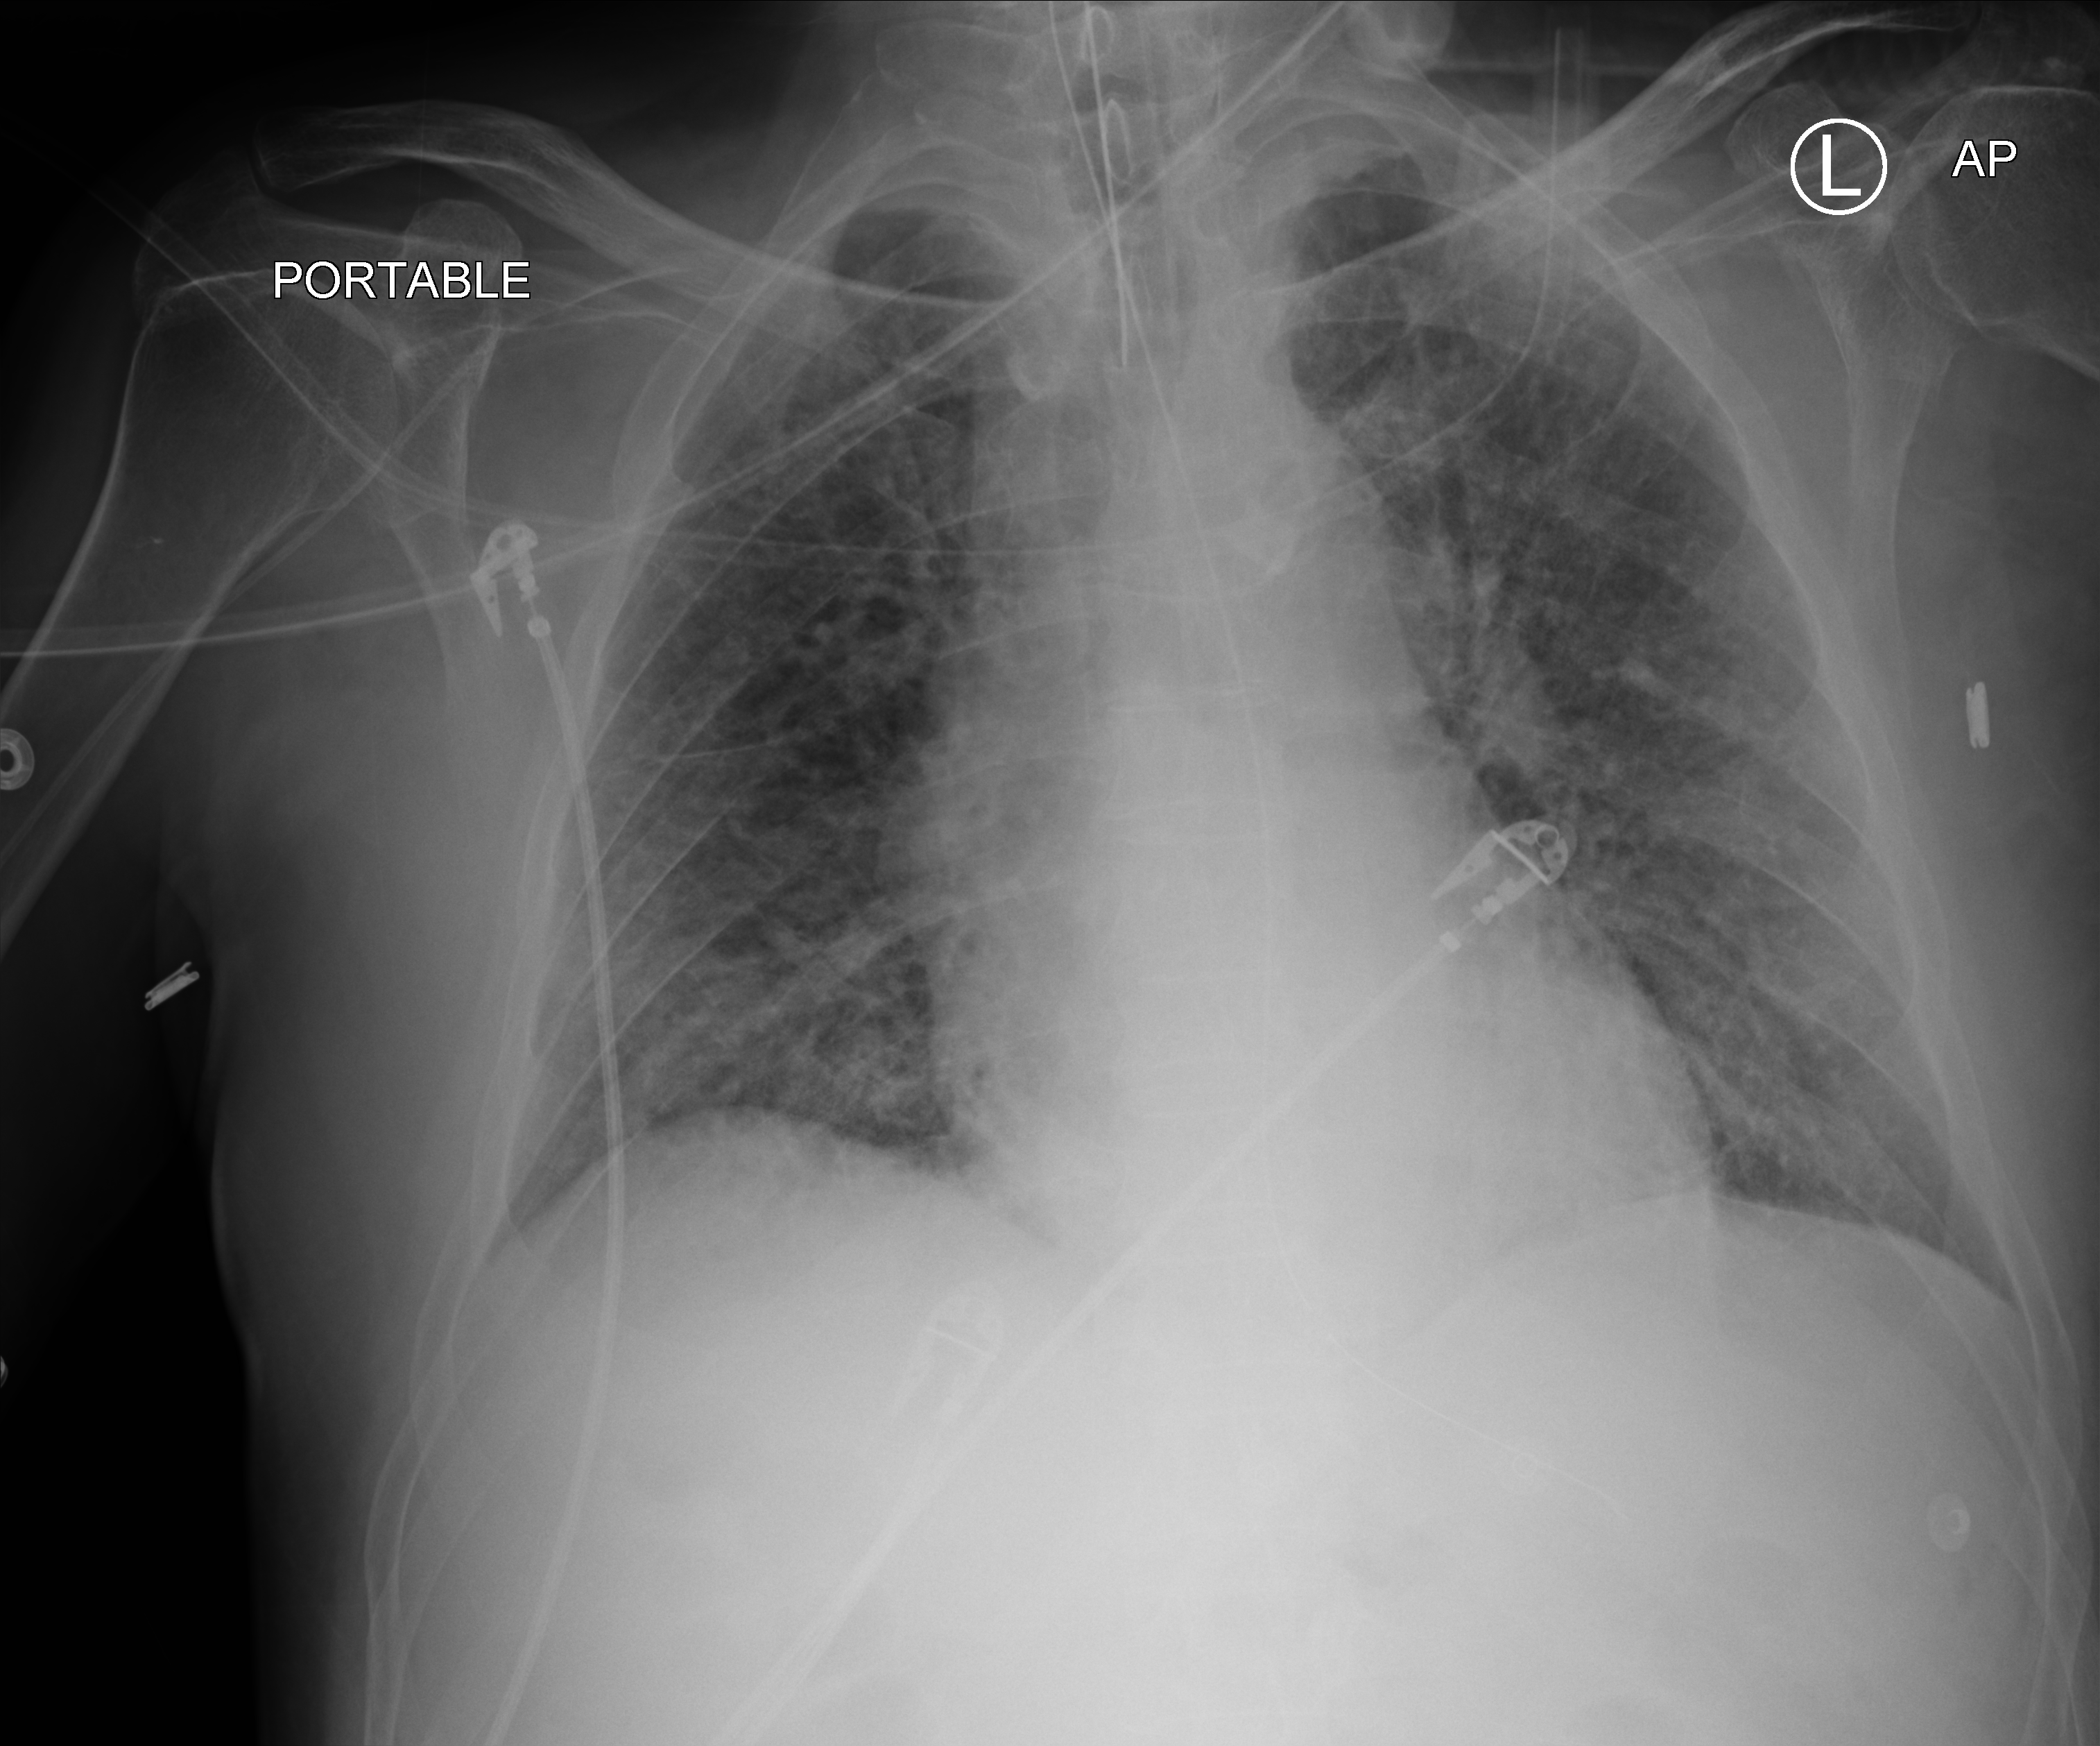
Chest X-ray (portable); anteroposterior (AP) projection. Patient hospitalised with COVID-19; male, aged 60–74 years.
Hospital-stay facts (about this admission, not read from this image; timing relative to this image not recorded):
- admitted to intensive care during this hospital stay: yes
- mechanically ventilated during this hospital stay: yes
- hypertension (admission record): no